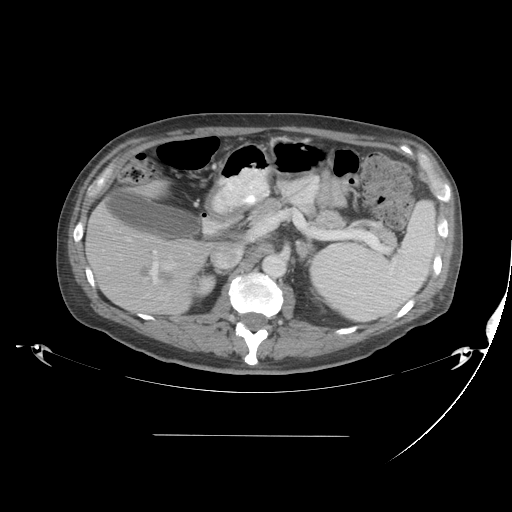
Contrast-enhanced abdominal CT, one axial slice. Position 23 of 48 along the scan axis. Intravenous contrast given. Soft-tissue window (W 400 / L 40 HU). 5 mm slice thickness. 512 × 512 image matrix. Male patient, age 65 years. Case-level facts recorded for this patient, not image findings: diagnosis: colorectal cancer liver metastases, imaged before liver resection; multiple liver metastases: yes; largest metastasis: 11 cm.
Outlined on this slice (expert manual segmentation):
- hepatic veins: bounding box <153,251,175,284> (left, top, right, bottom; pixels)
- liver: <88,185,213,316>
- planned liver remnant (the part of the liver to remain after resection): <145,184,160,196>
- portal vein (with intrahepatic branches): <124,237,157,274>
- liver metastasis: <140,269,170,281>